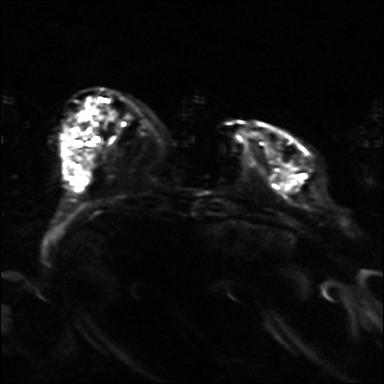
Breast MRI, one axial slice; position 9 of 36 along the scan axis; diffusion-weighted series; image 2 of 4 stored at this slice position (different b-values; order by instance number); 3 T; 4 mm slice thickness; 384 × 384 image matrix, field of view 320 × 320 mm. Female patient.
Annotated regions visible in this slice (outlined manually by an expert reader):
- tumour on diffusion-weighted imaging: bounding box [x1, y1, x2, y2] px = [282, 163, 293, 179]